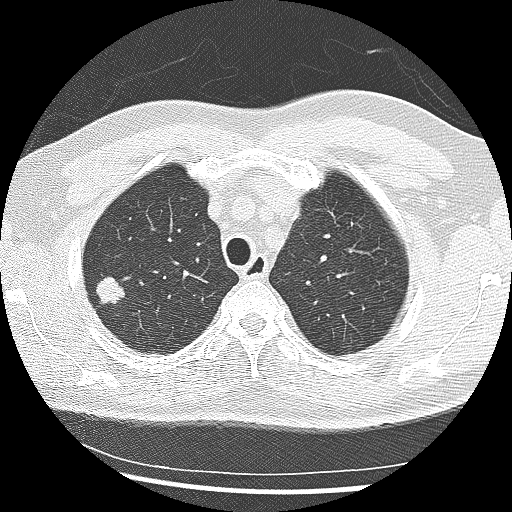
Low-dose screening chest CT, one axial slice; slice 212 of 265 in the series (ordered by position); reconstruction kernel LUNG; 120 kVp; lung window (W 1500 / L -600 HU); 2.5 mm slice thickness; 512 × 512 image matrix.
Outlined on this slice (outlined manually by an expert reader):
- lesion 1 (tumor, upper lobe of right lung): bounding box [x1, y1, x2, y2] px = [97, 277, 125, 304]